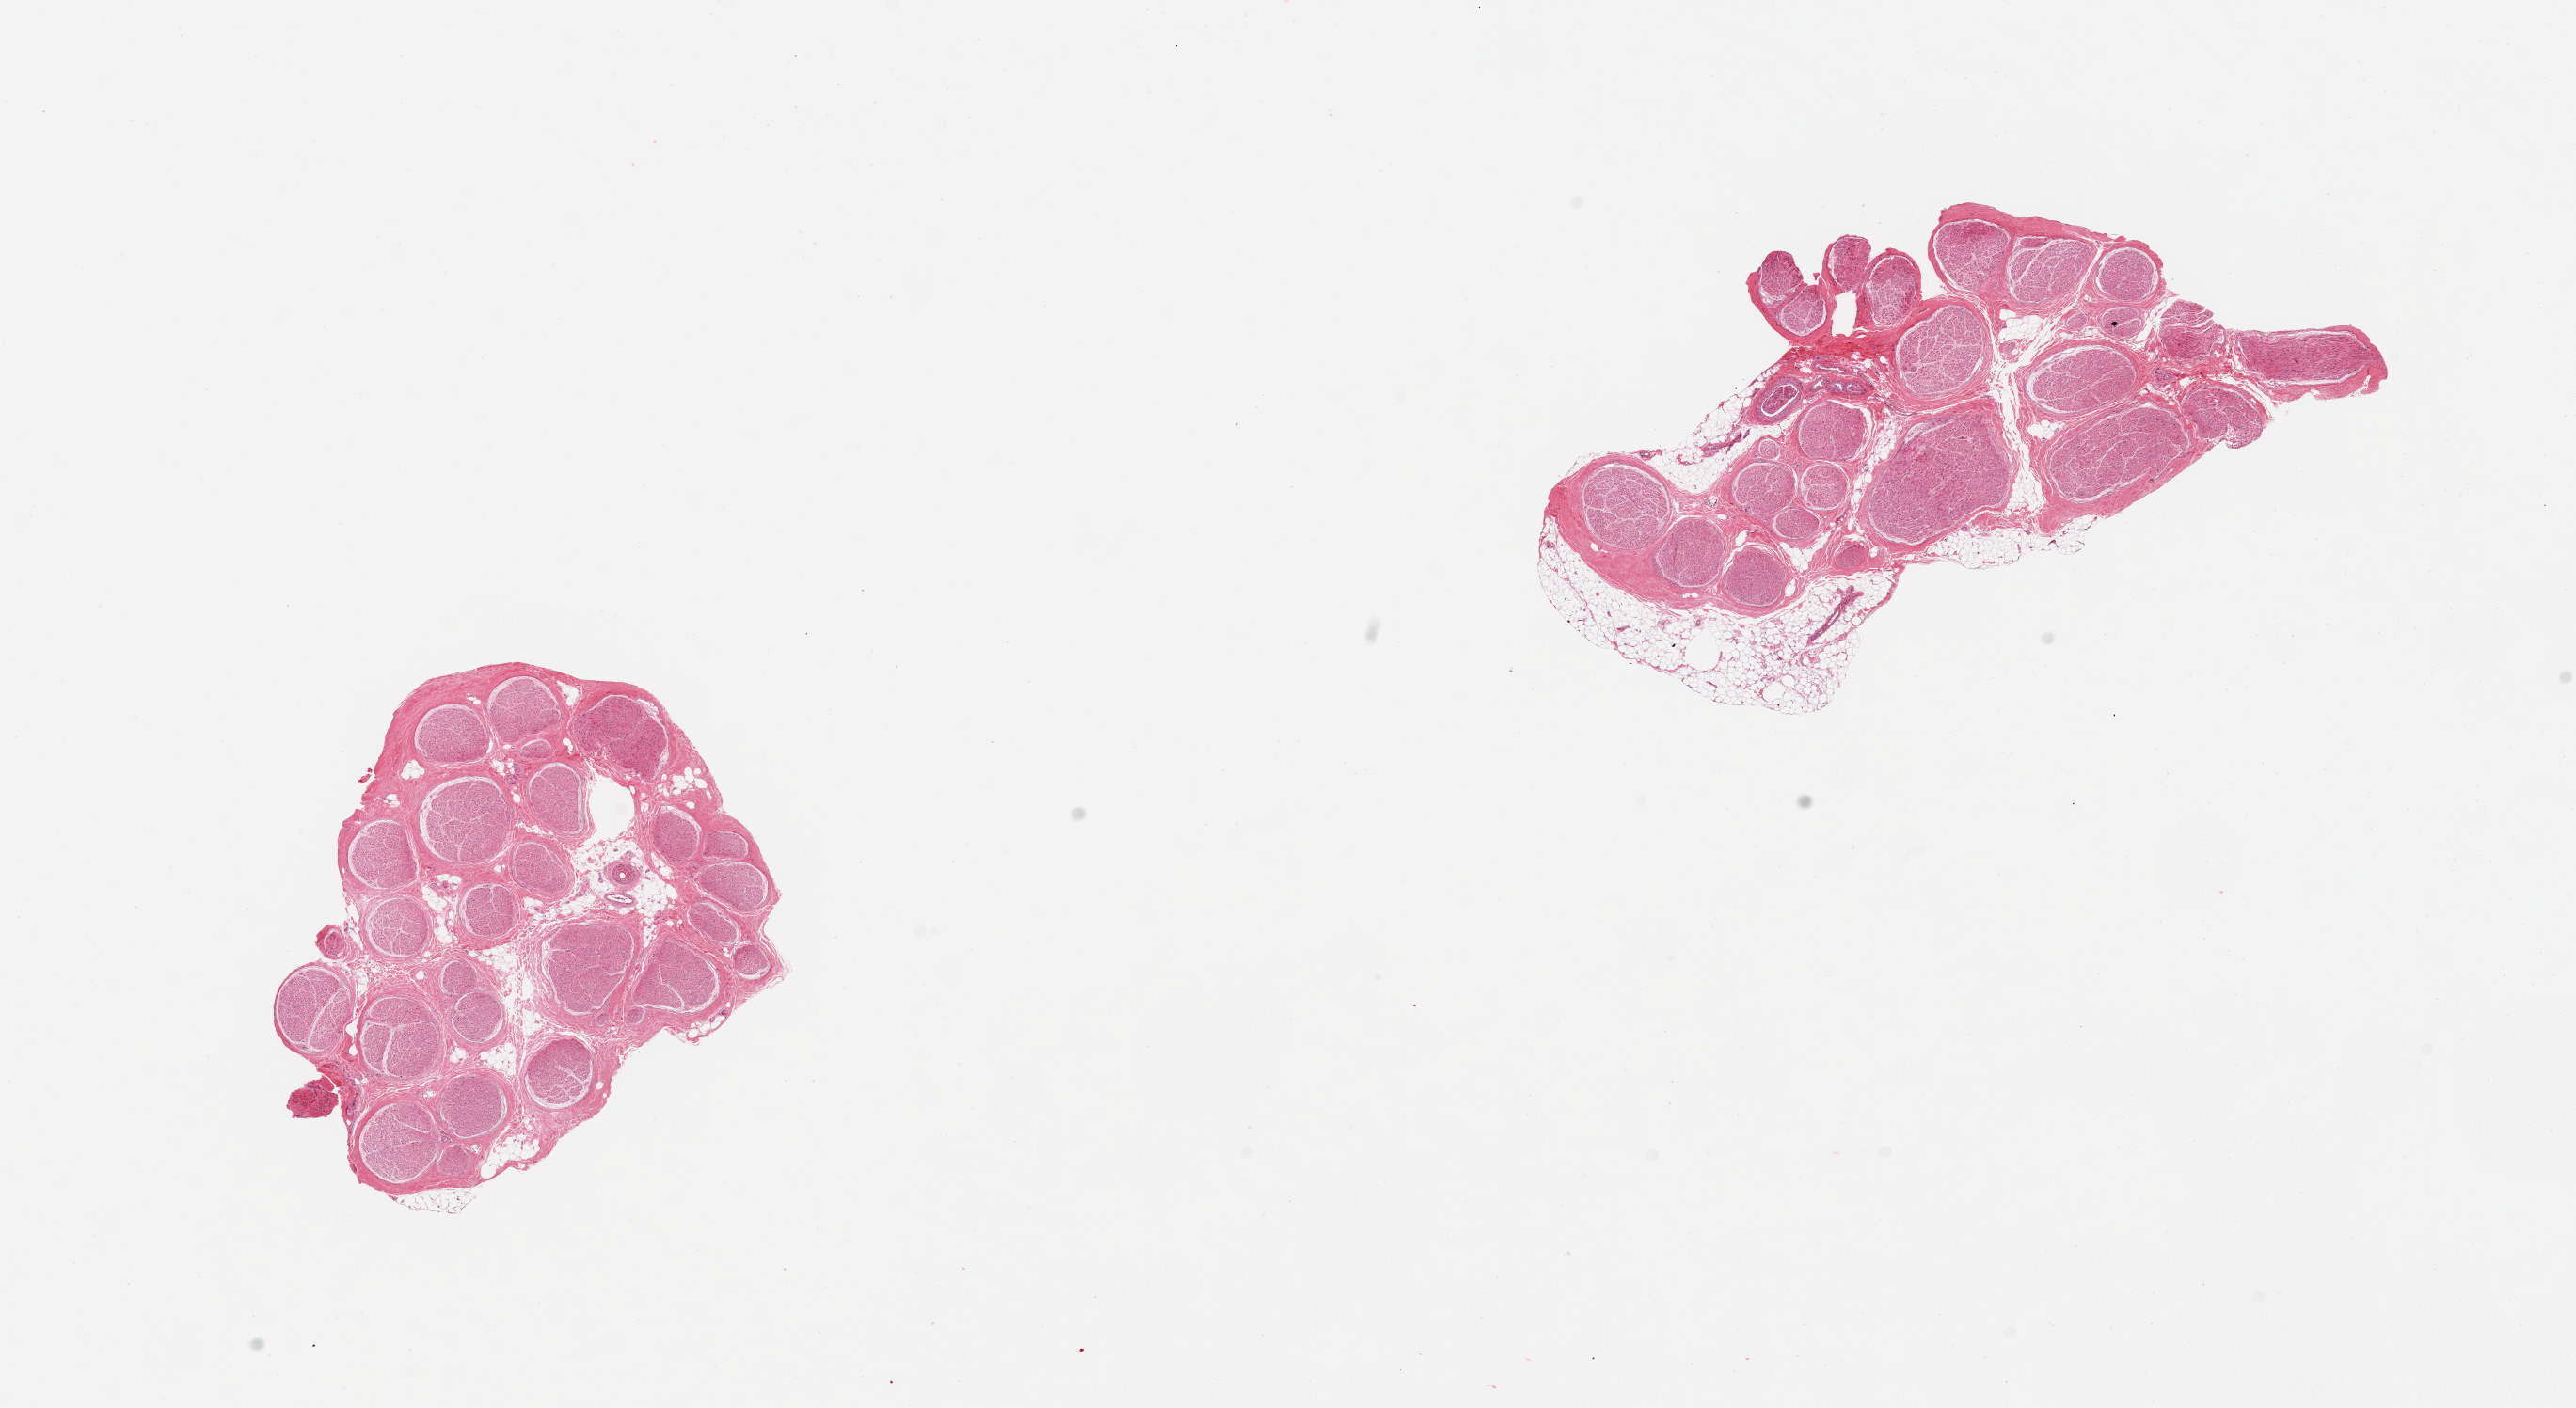
Whole-slide image, haematoxylin and eosin stain — a low-resolution overview of the entire scanned area, about 21.7 x 11.8 mm (from a 20x scan), PAXgene-fixed, paraffin-embedded tissue, section of tibial nerve (target tissue), donor tissue sample. Male donor.
Reviewer comment on this tissue sample: 2 pieces; includes 10-20% attached (2.7mm) and internal fat.